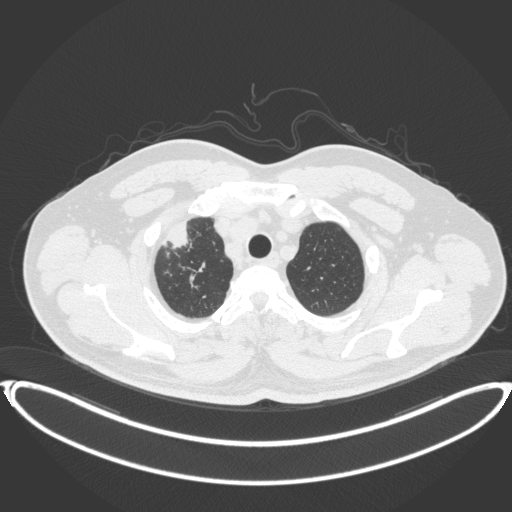
Chest CT, one axial slice. Position 339 of 399 along the scan axis. Reconstruction kernel B31f. Lung window (W 1500 / L -600 HU). 512 × 512 image matrix, field of view 445 × 445 mm. Male patient, age 53 years. From the clinical record (not read from this slice): clinical TNM (as recorded): T2a N0 M0.
Structures marked on this image (bounding box drawn by a radiologist):
- lung tumour (recorded histology: adenocarcinoma): bounding box [x1, y1, x2, y2] px = [167, 219, 195, 253]